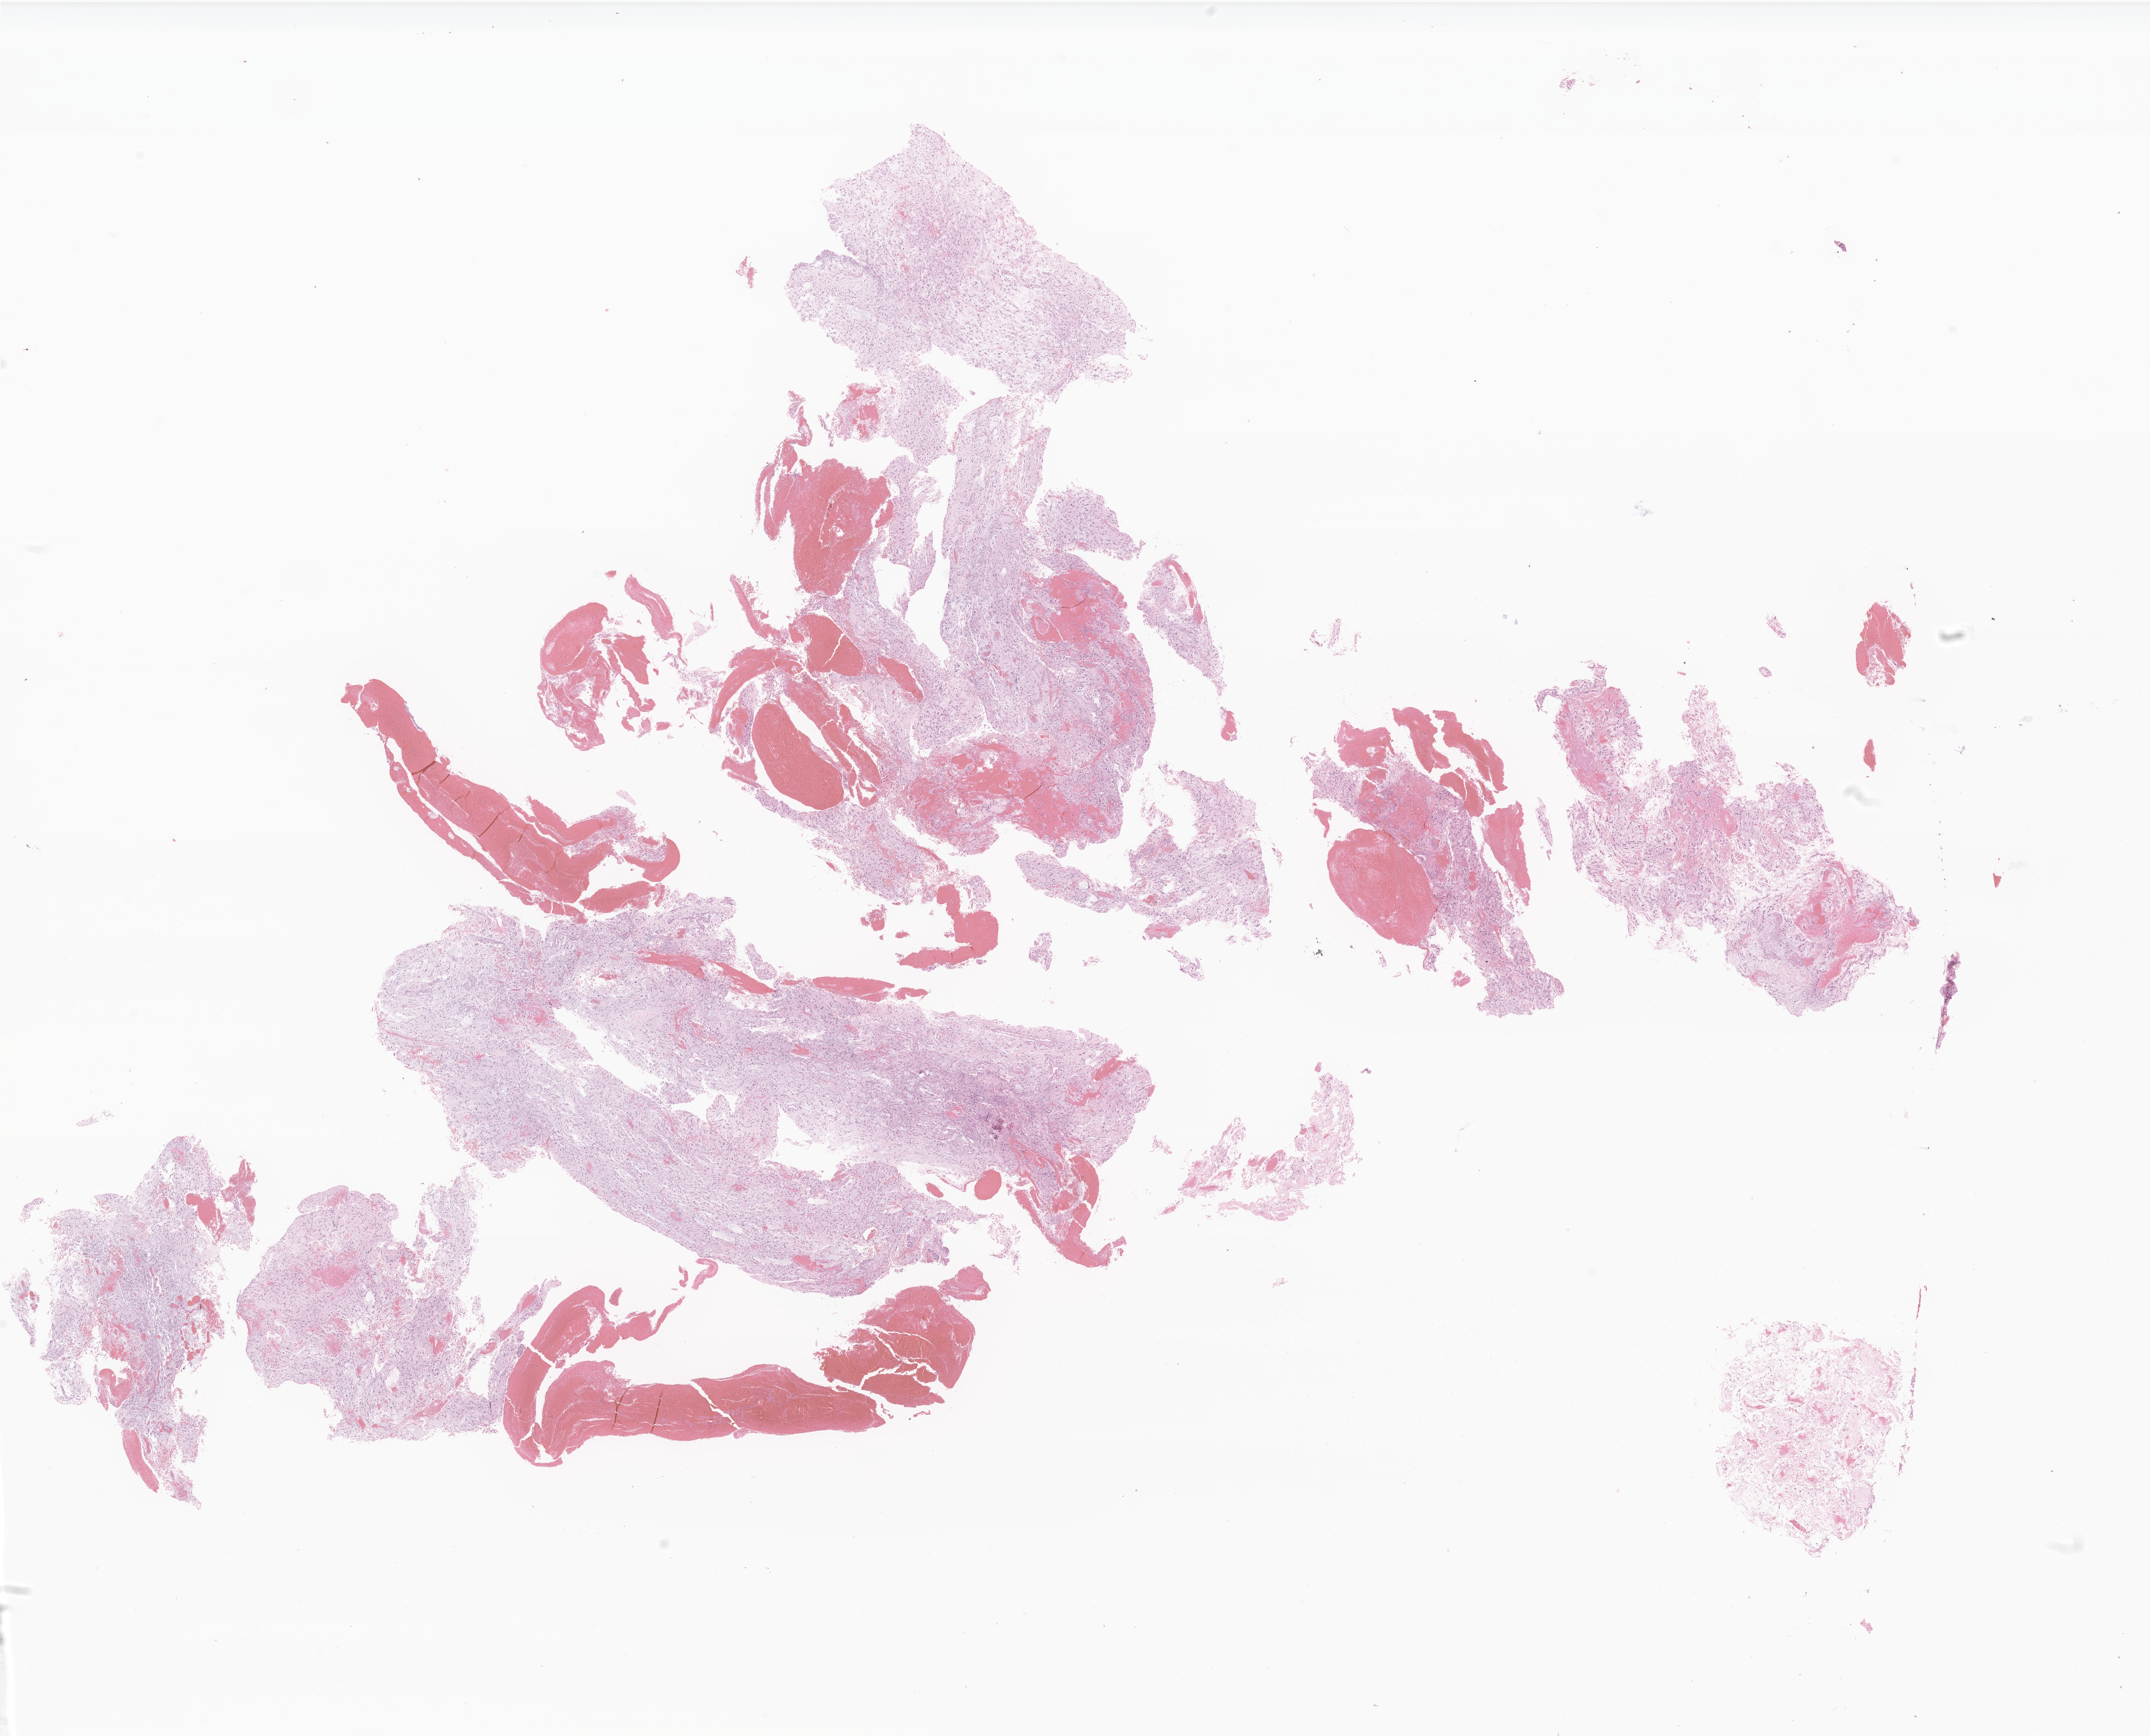
Haematoxylin and eosin whole-slide image of tumor tissue from the brain, shown as a low-resolution overview of the whole scanned area (about 22.9 x 18.5 mm). Formalin-fixed, paraffin-embedded (FFPE) tissue. Female patient, age 203 months (16 years 11 months).
Diagnosis: Pilocytic astrocytoma.